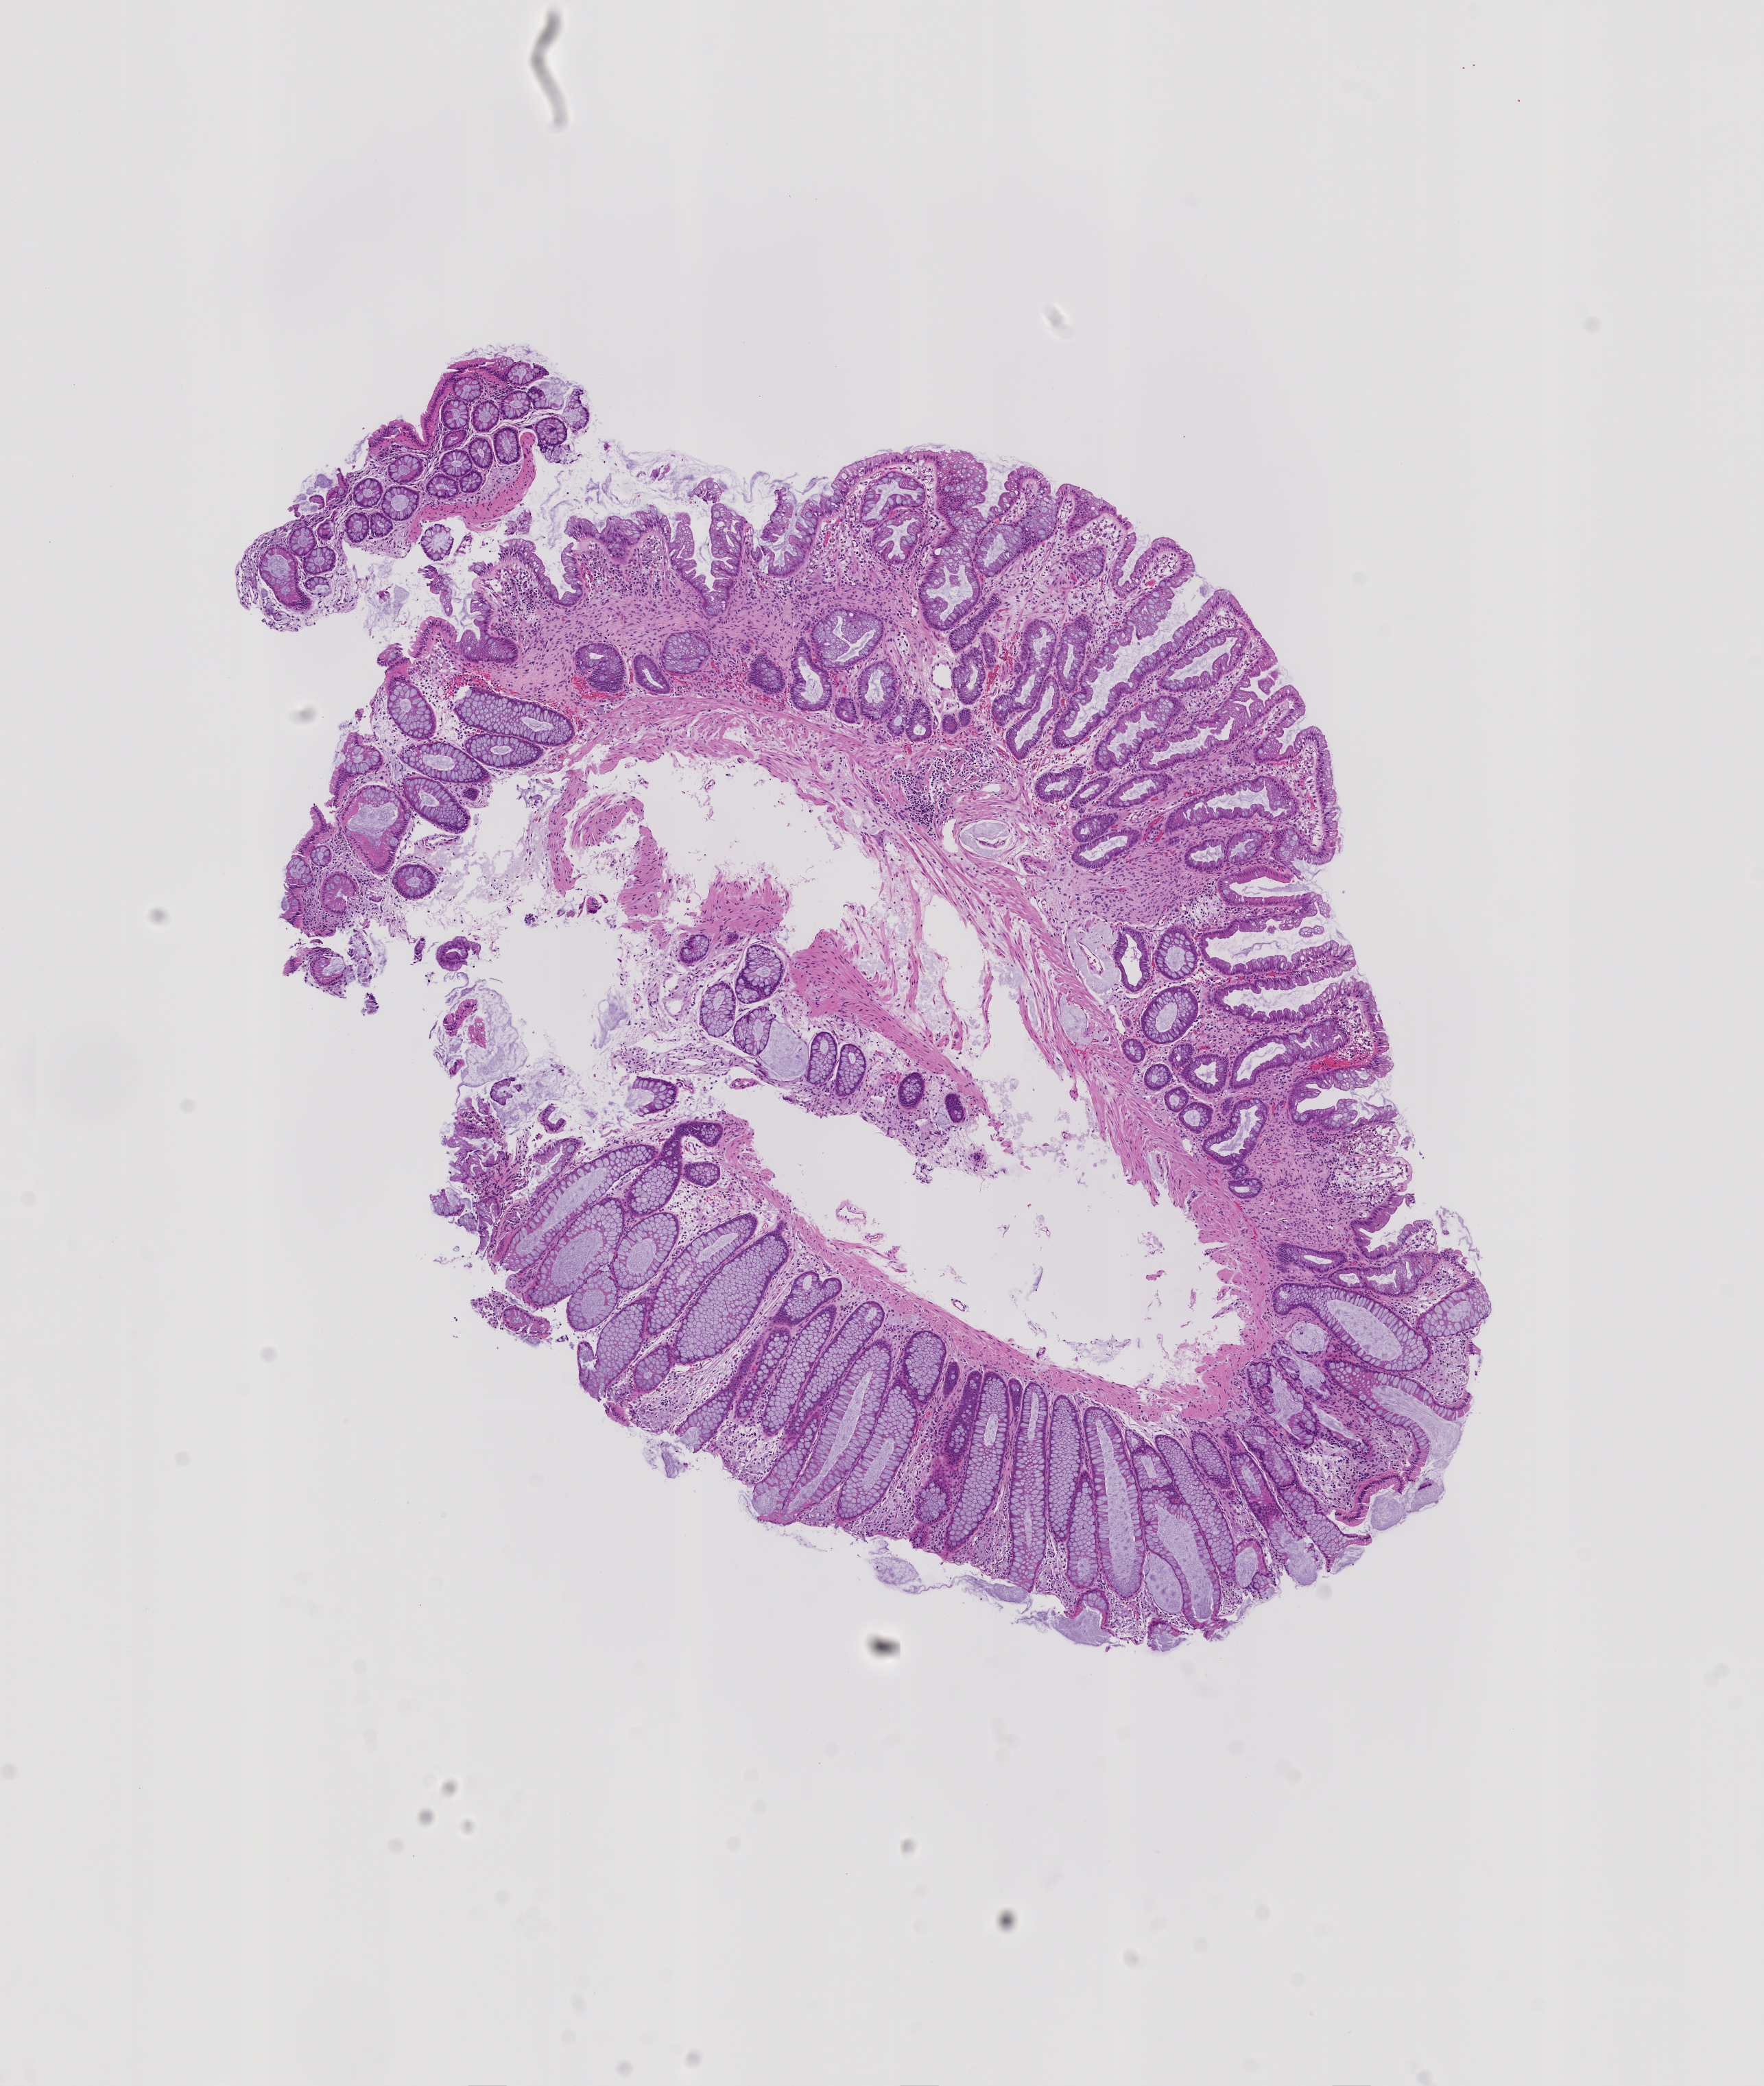
Hematoxylin and eosin (H&E) whole-slide image of a colon biopsy, low-resolution overview of the scanned area, about 5.1 x 6.1 mm, formalin-fixed paraffin-embedded section, sigmoid colon. Female patient.
Lesion category (as recorded): premalignant.